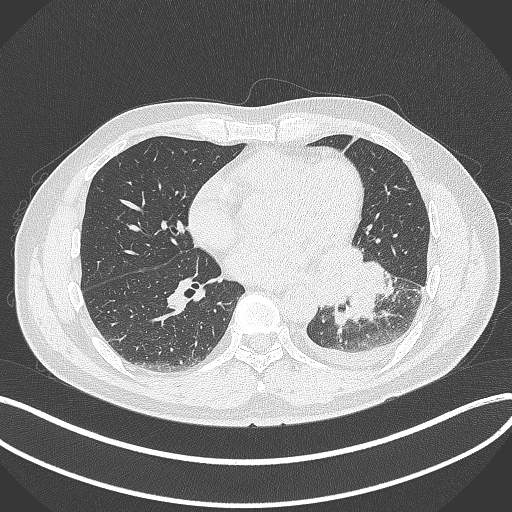
Chest CT, one axial slice. Position 155 of 342 along the scan axis. Lung window (W 1500 / L -600 HU). 1 mm slice thickness. 512 × 512 image matrix. Male patient, age 58 years. From the clinical record (not read from this slice): clinical TNM (as recorded): T3 N1 M1b; histopathological grade: G3.
Outlined on this slice (rectangle marked by the reading radiologist):
- lung tumour (recorded histology: small cell carcinoma): bounding box [x1, y1, x2, y2] px = [321, 242, 398, 328]